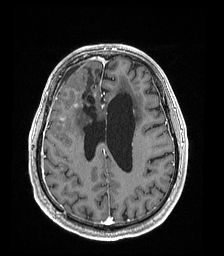
Brain MRI from a brain-tumour surgery series, one axial slice. Slice 67 of 192 in the series (ordered by position). T1-weighted post-contrast. 224 × 256 image matrix, field of view 224 × 256 mm. Case-level facts recorded for this patient, not image findings: histopathology: Astrocytoma; WHO grade: 4; IDH mutation: yes; tumour location: Right Frontal.
Outlined on this slice (expert manual segmentation):
- previous resection cavity: bounding box <84,67,91,115> (left, top, right, bottom; pixels)